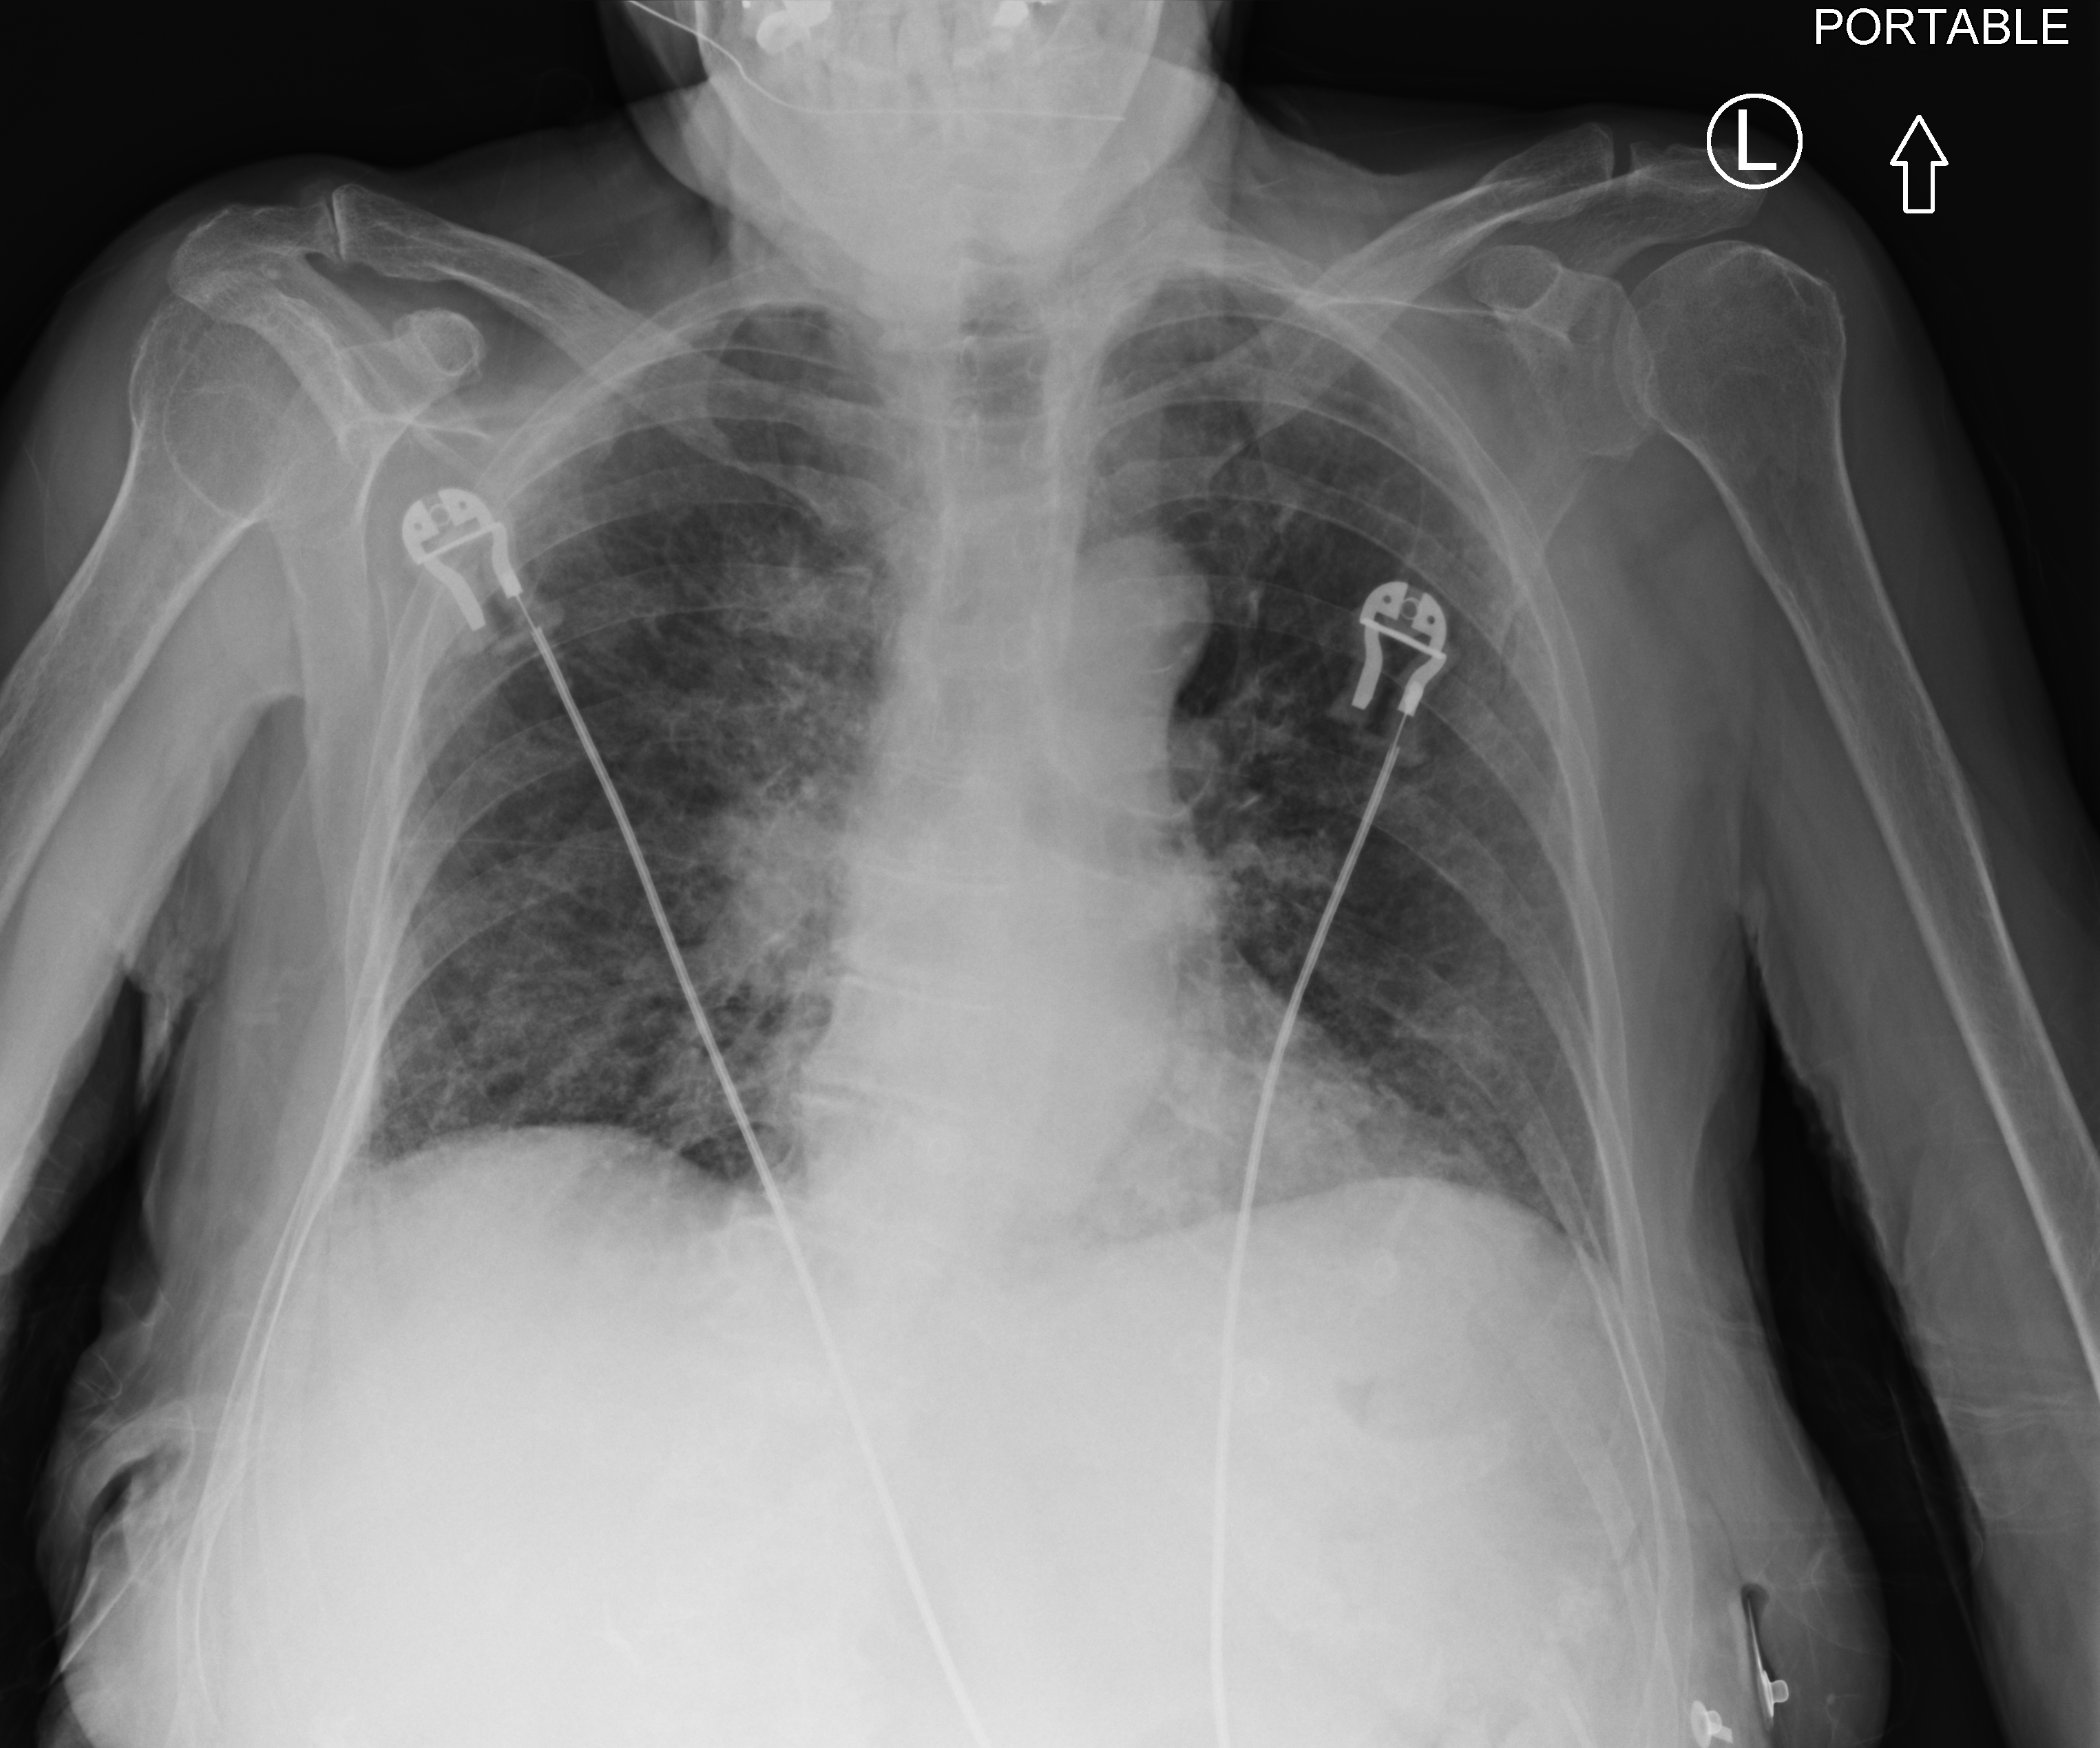
Portable chest radiograph; anteroposterior (AP) projection. Female patient hospitalised with COVID-19, age 75–90 years.
Admission-level facts for this patient (not findings on this image; timing relative to this image not recorded): chronic kidney disease (admission record): no; length of hospital stay: 13 days.